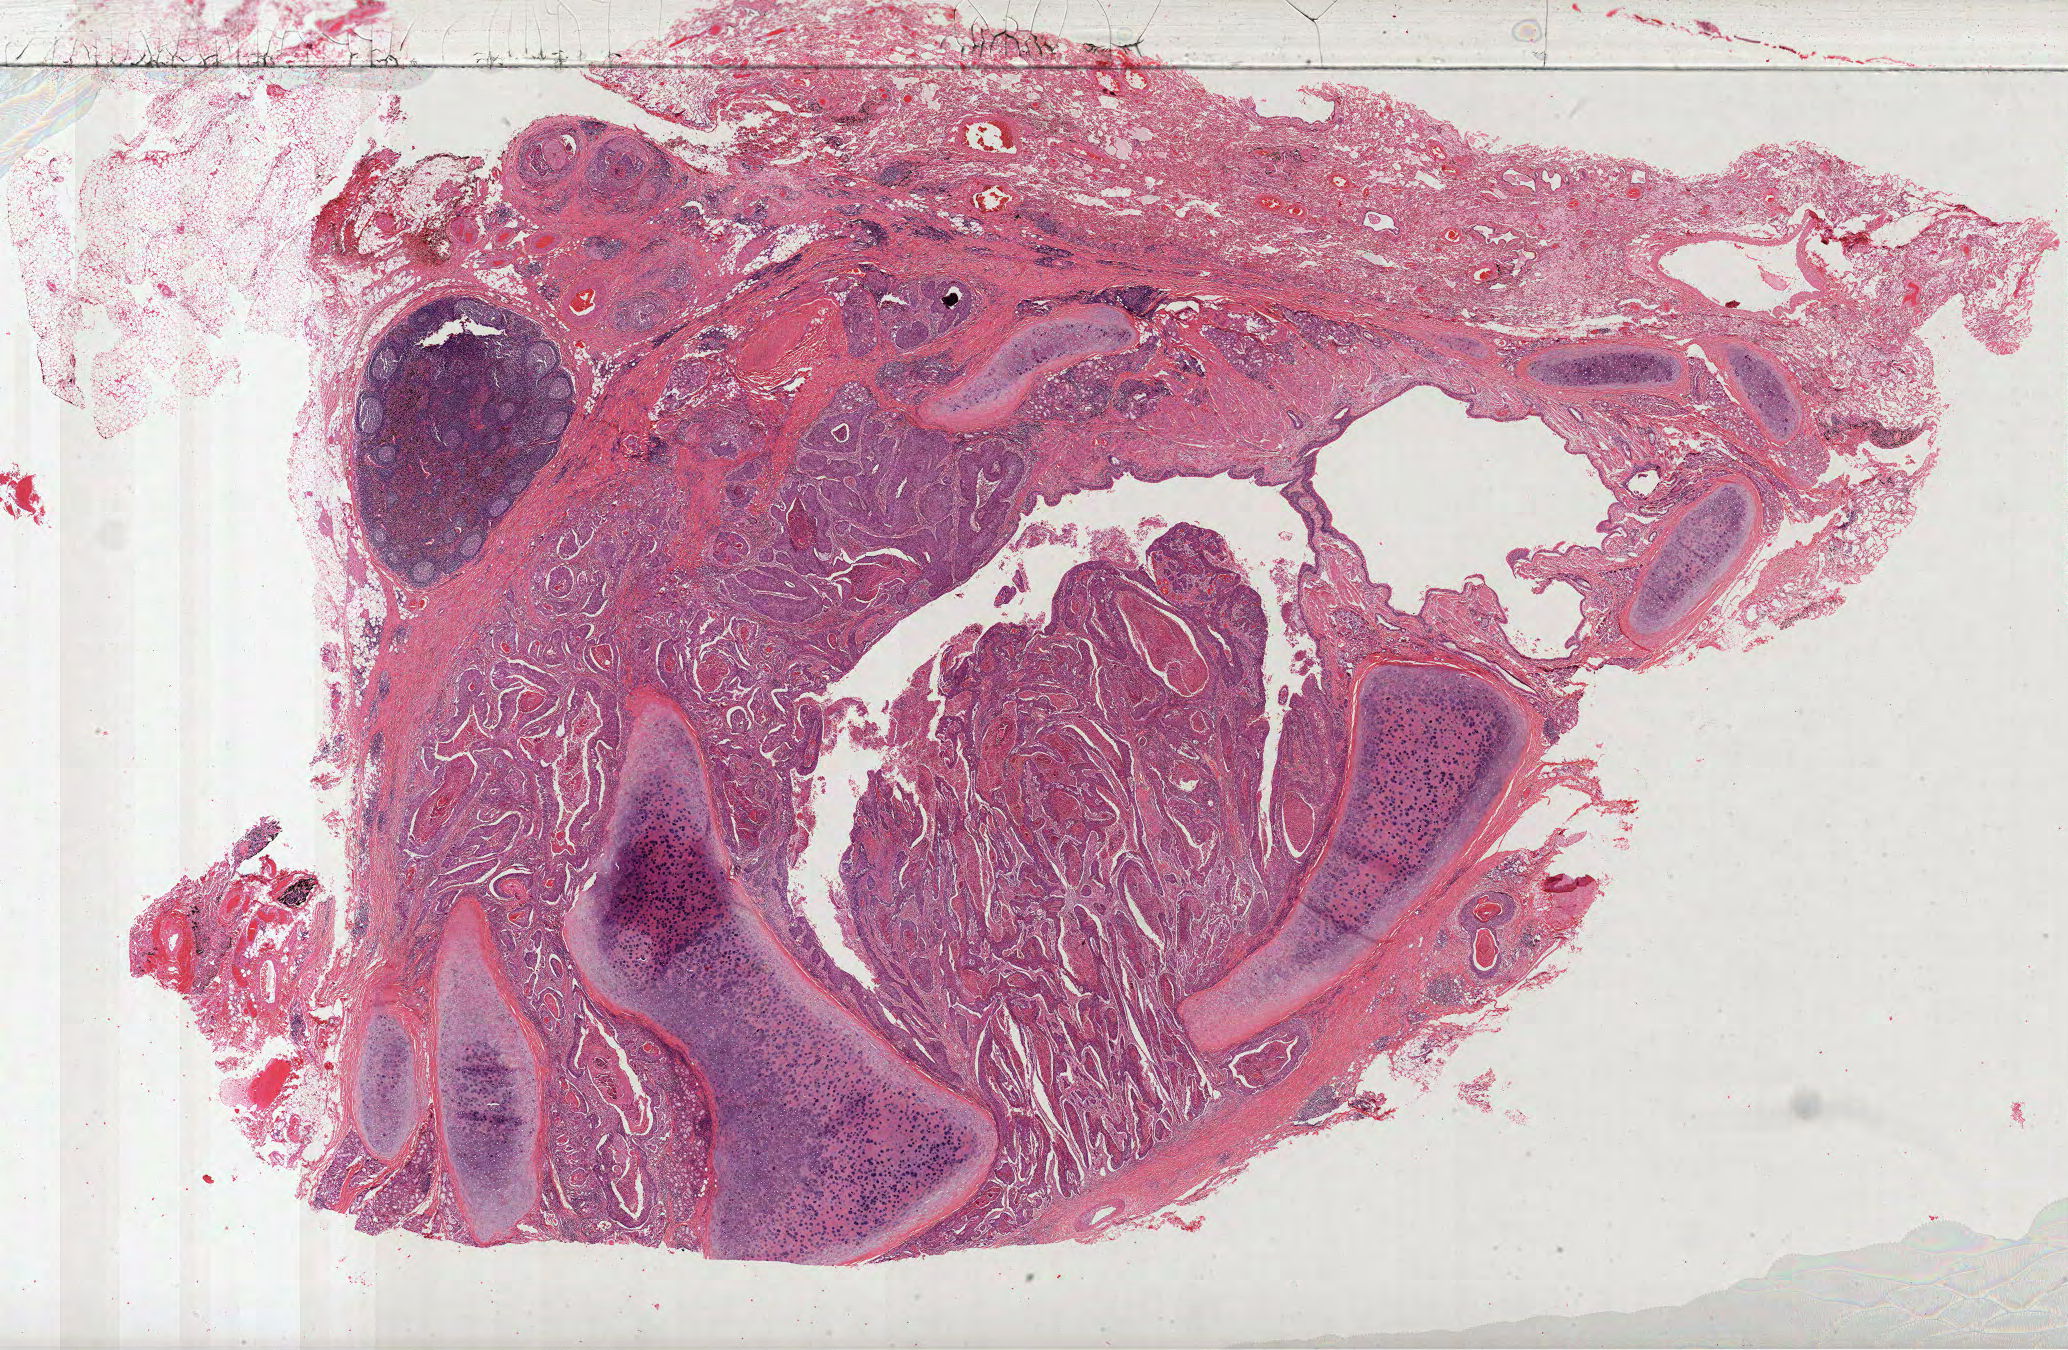
Digitized H&E tissue section (whole slide) — low-resolution overview of the scanned area, about 33.4 x 21.8 mm; formalin-fixed paraffin-embedded (FFPE) diagnostic section; lung, primary tumour sample. Patient: male, age at initial diagnosis 64 years.
AJCC pathologic stage: IIIA. Laterality: right. Histologic diagnosis: Squamous cell carcinoma, NOS. TNM: T3 N1 M0.